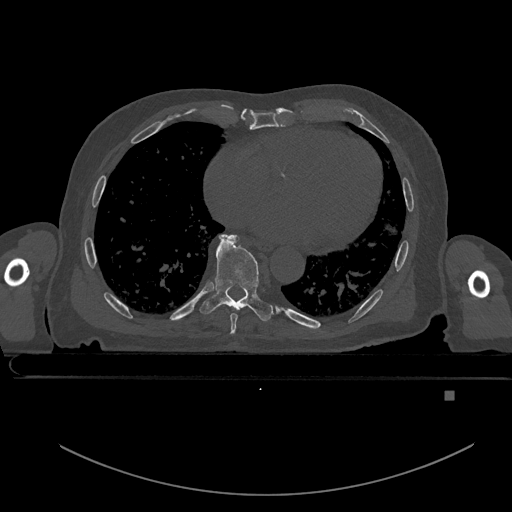
CT including the spine, one axial slice; position 213 of 969 along the scan axis; bone window (W 1800 / L 400 HU); 0.5 mm slice thickness; 512 × 512 image matrix, field of view 456 × 456 mm. Male patient, age 82 years. From the clinical record (not read from this slice): primary cancer: prostate.
Outlined on this slice (semi-automatically segmented with operator editing):
- T7 vertebra: bounding box (x1, y1, x2, y2) in pixels: (227, 235, 238, 334)
- T8 vertebra: (199, 234, 274, 321)